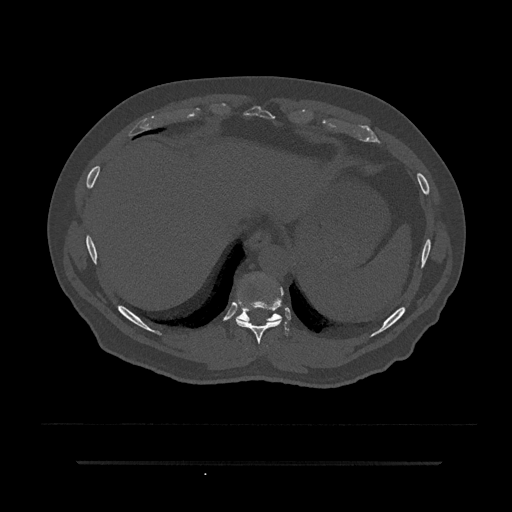
CT including the spine, one axial slice. Position 358 of 797 along the scan axis. Reconstruction kernel Br40s/3. 120 kVp. Bone window (W 1800 / L 400 HU). 0.5 mm slice thickness. 512 × 512 image matrix. Patient: male, 59 years. Case-level facts recorded for this patient, not image findings: primary cancer: bile ducts.
Outlined on this slice (semi-automatic segmentation, software-assisted and operator-edited):
- T10 vertebra: box from (x=236, y=306) to (x=289, y=335) px
- T9 vertebra: (x=236, y=280)–(x=284, y=344)